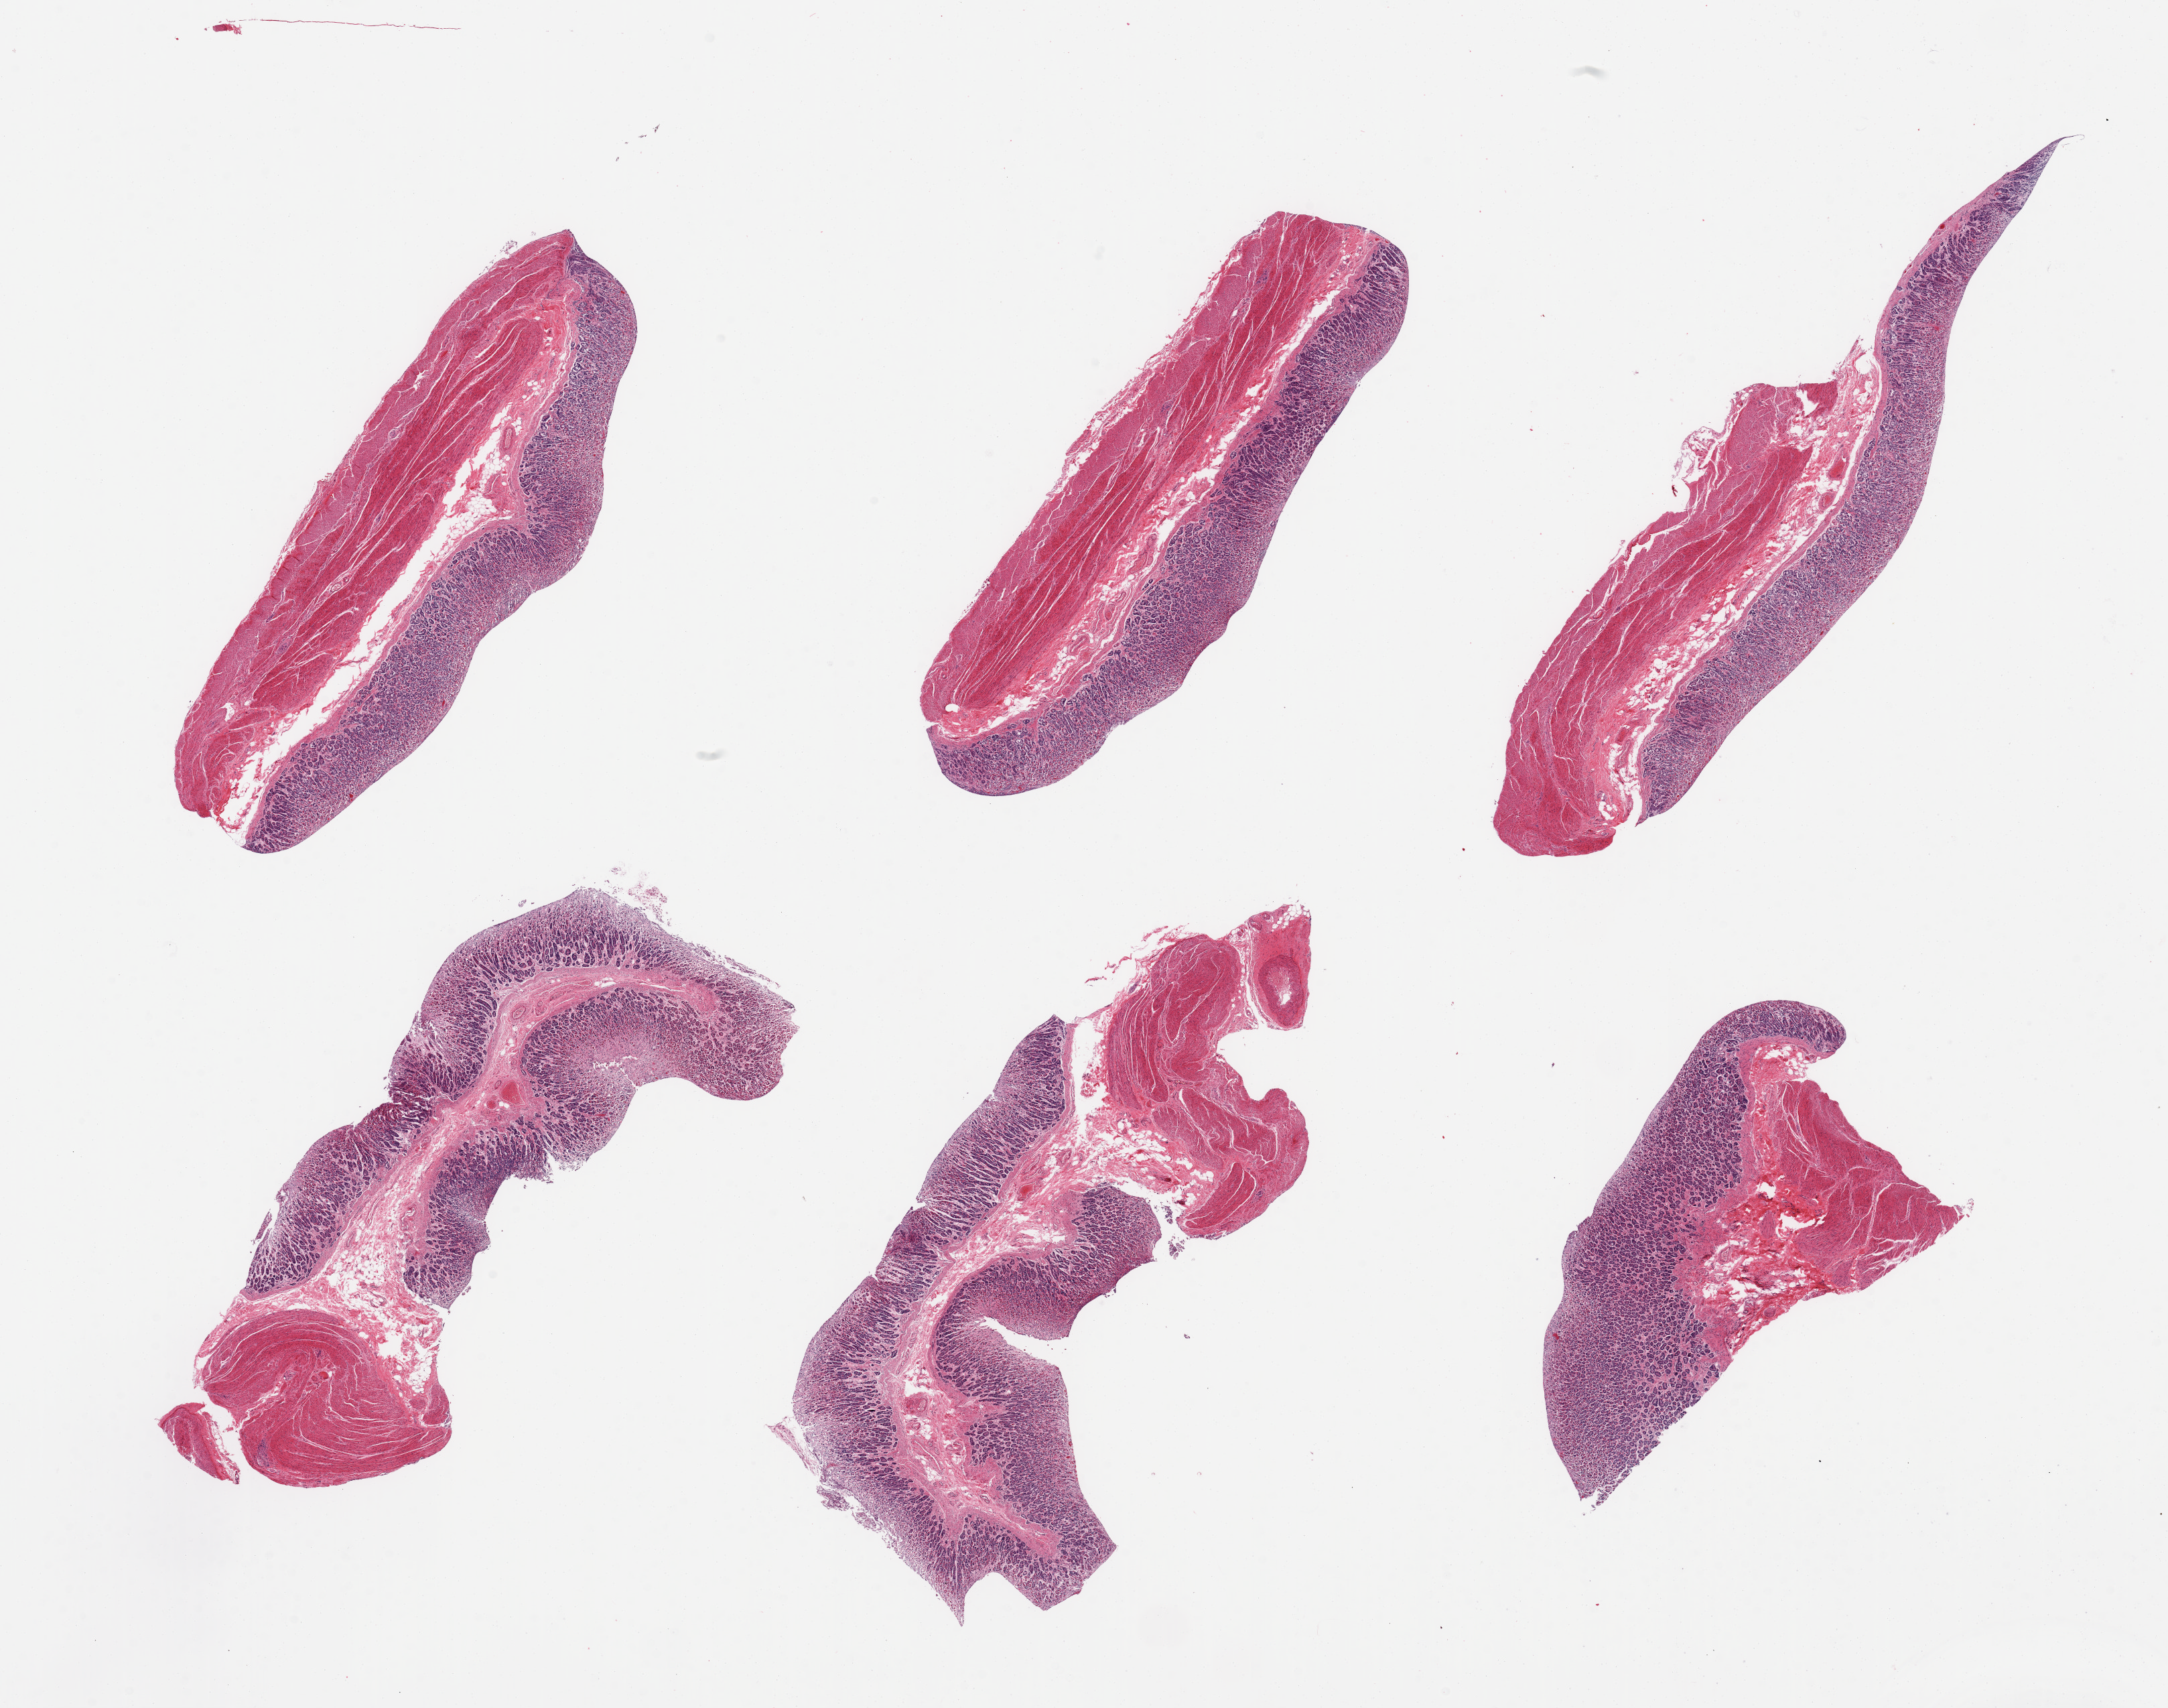
Whole-slide image, haematoxylin and eosin stain, brightfield — a low-resolution overview of the entire scanned area, about 25.6 x 20.2 mm (from a 20x scan), PAXgene-fixed, paraffin-embedded tissue, sampled site (target tissue): stomach, donor tissue sample.
Pathologist's review note for this sample: 6 pieces, mucosa up to ~1mm, ~40% of thickness.